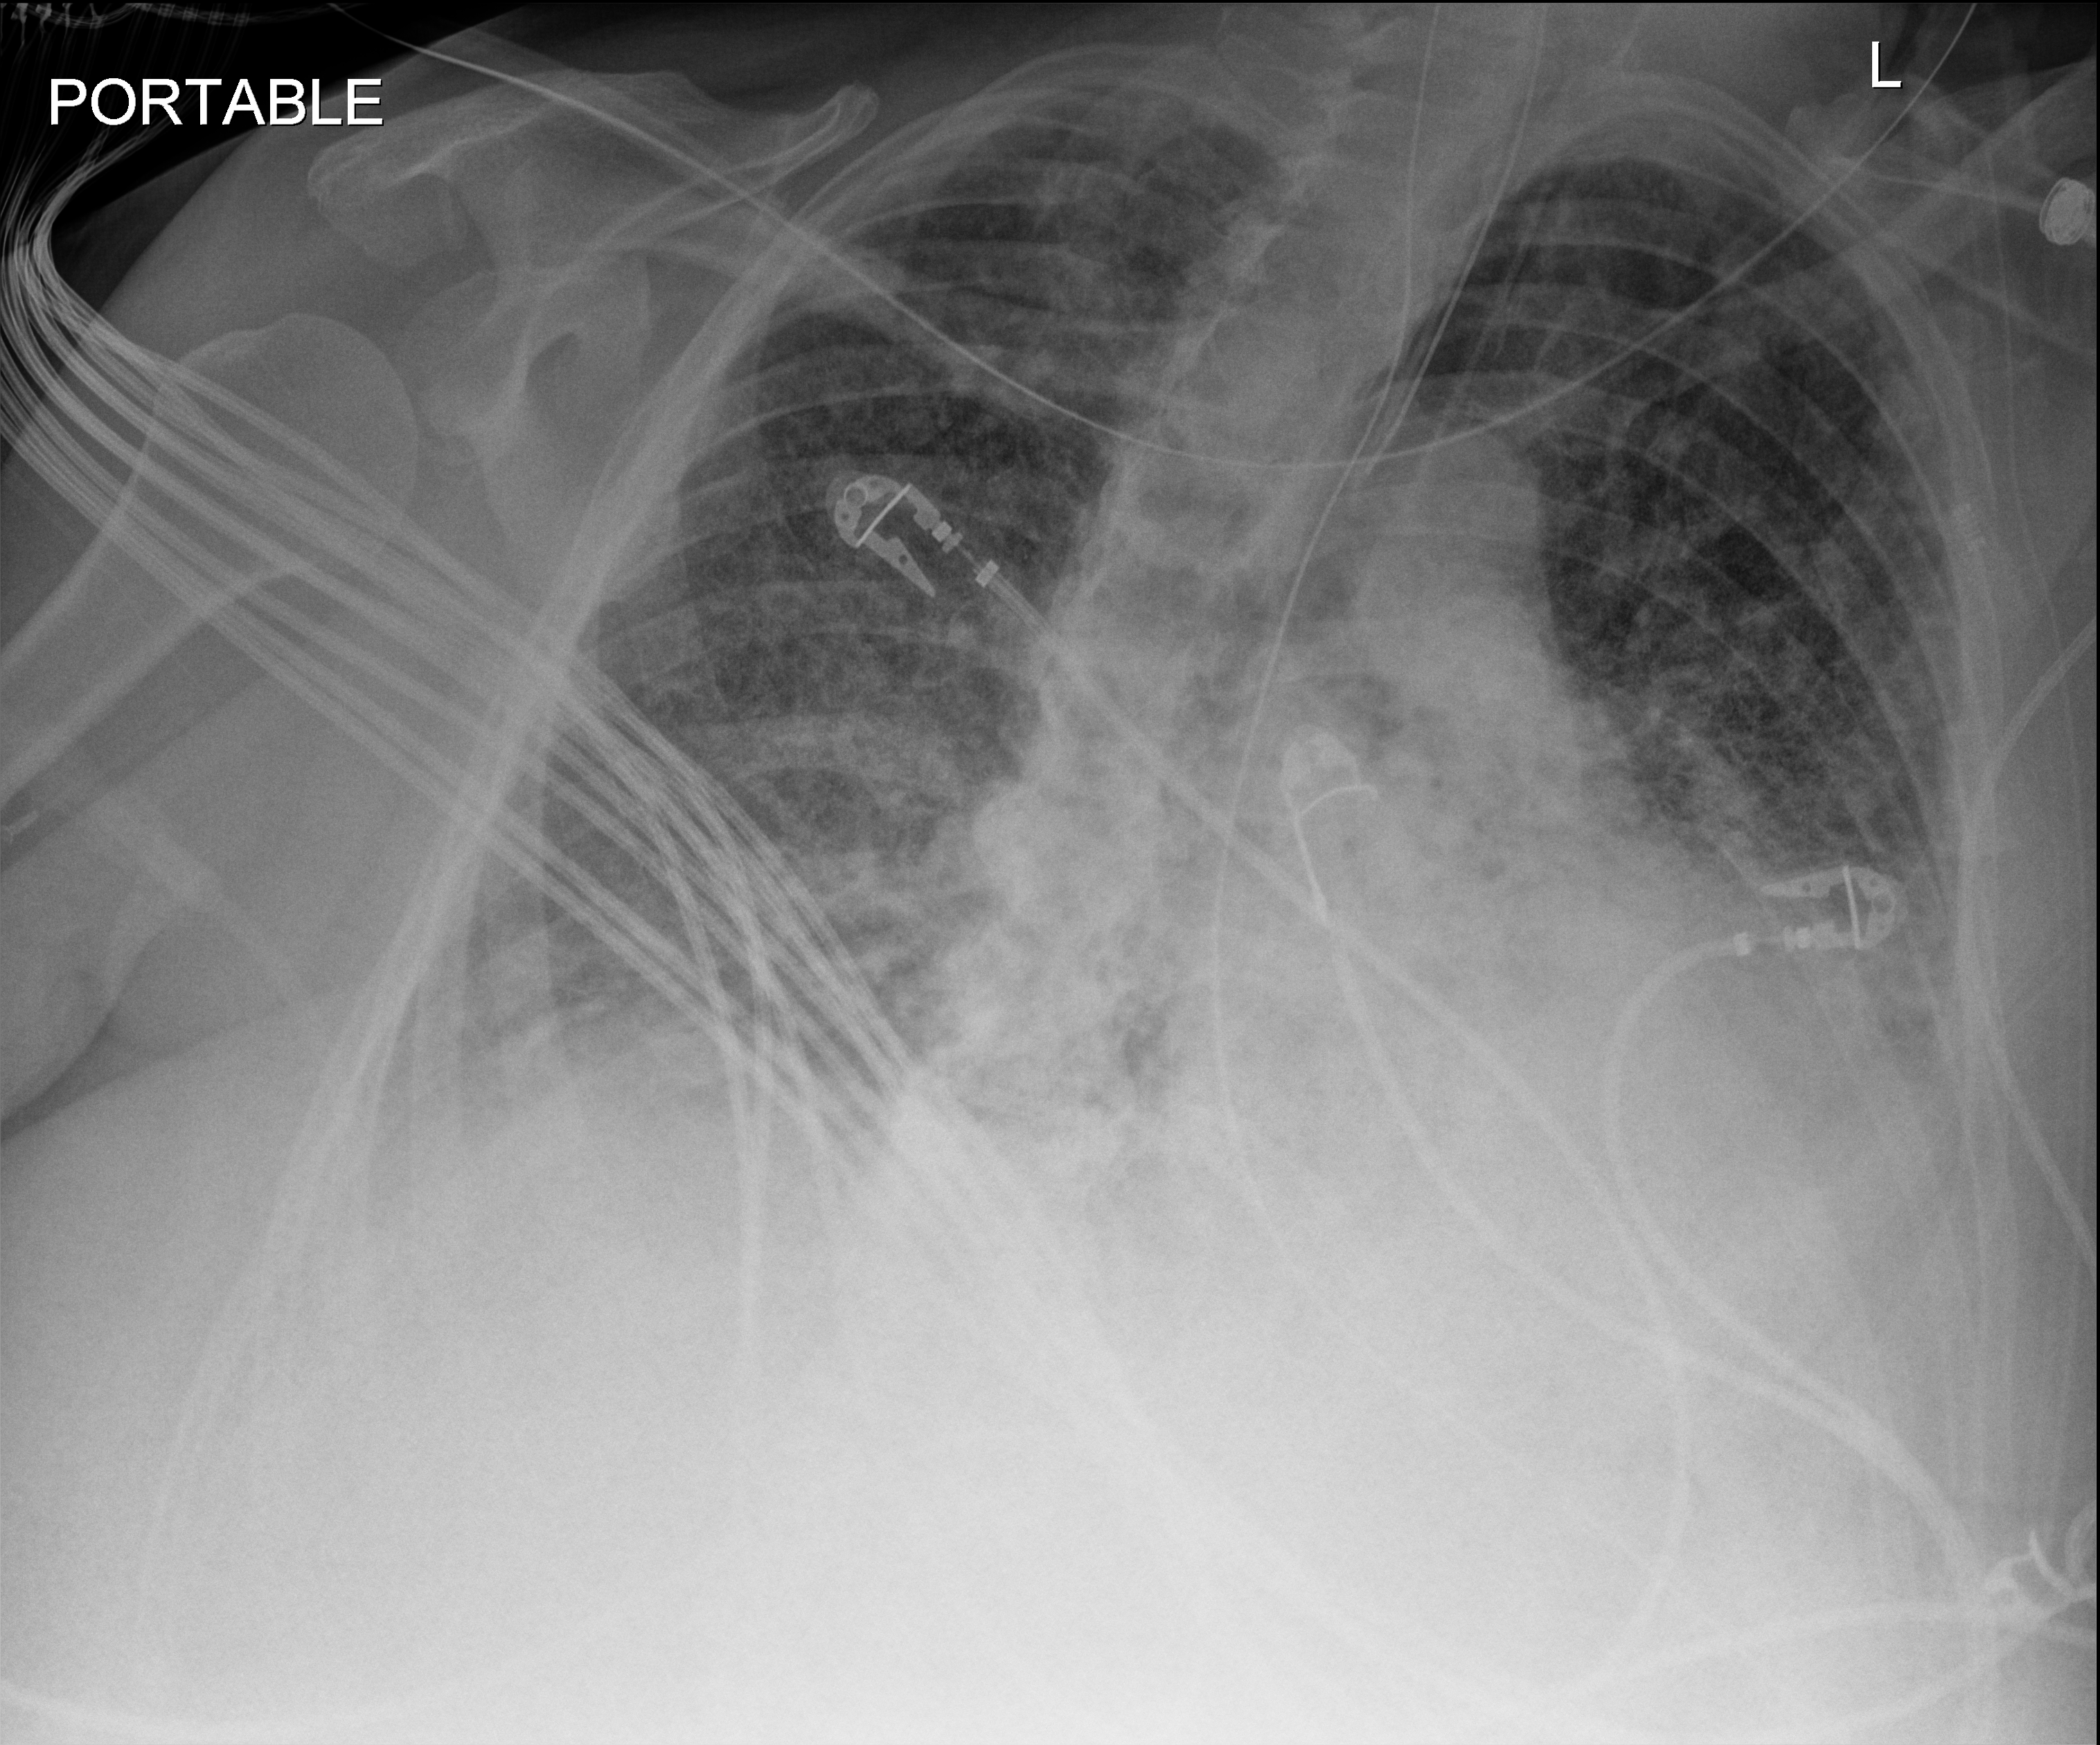
Portable chest radiograph, anteroposterior (AP) projection. Patient hospitalised with COVID-19, aged 18–59 years.
Hospital-stay facts (about this admission, not read from this image; timing relative to this image not recorded):
- admitted to intensive care during this hospital stay: yes
- mechanically ventilated during this hospital stay: yes